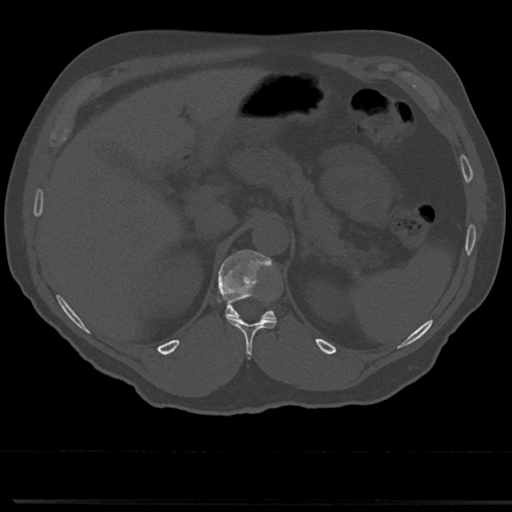
CT including the spine, one axial slice. Slice 175 of 817 in the series (ordered by position). 120 kVp. Bone window (W 1800 / L 400 HU). 0.5 mm slice thickness. 512 × 512 image matrix. Patient: male, 61 years. From the clinical record (not read from this slice): primary cancer: prostate.
Structures marked on this image (semi-automatically segmented with operator editing):
- T11 vertebra: box from (x=228, y=318) to (x=276, y=359) px
- T12 vertebra: (x=216, y=250)–(x=281, y=322)